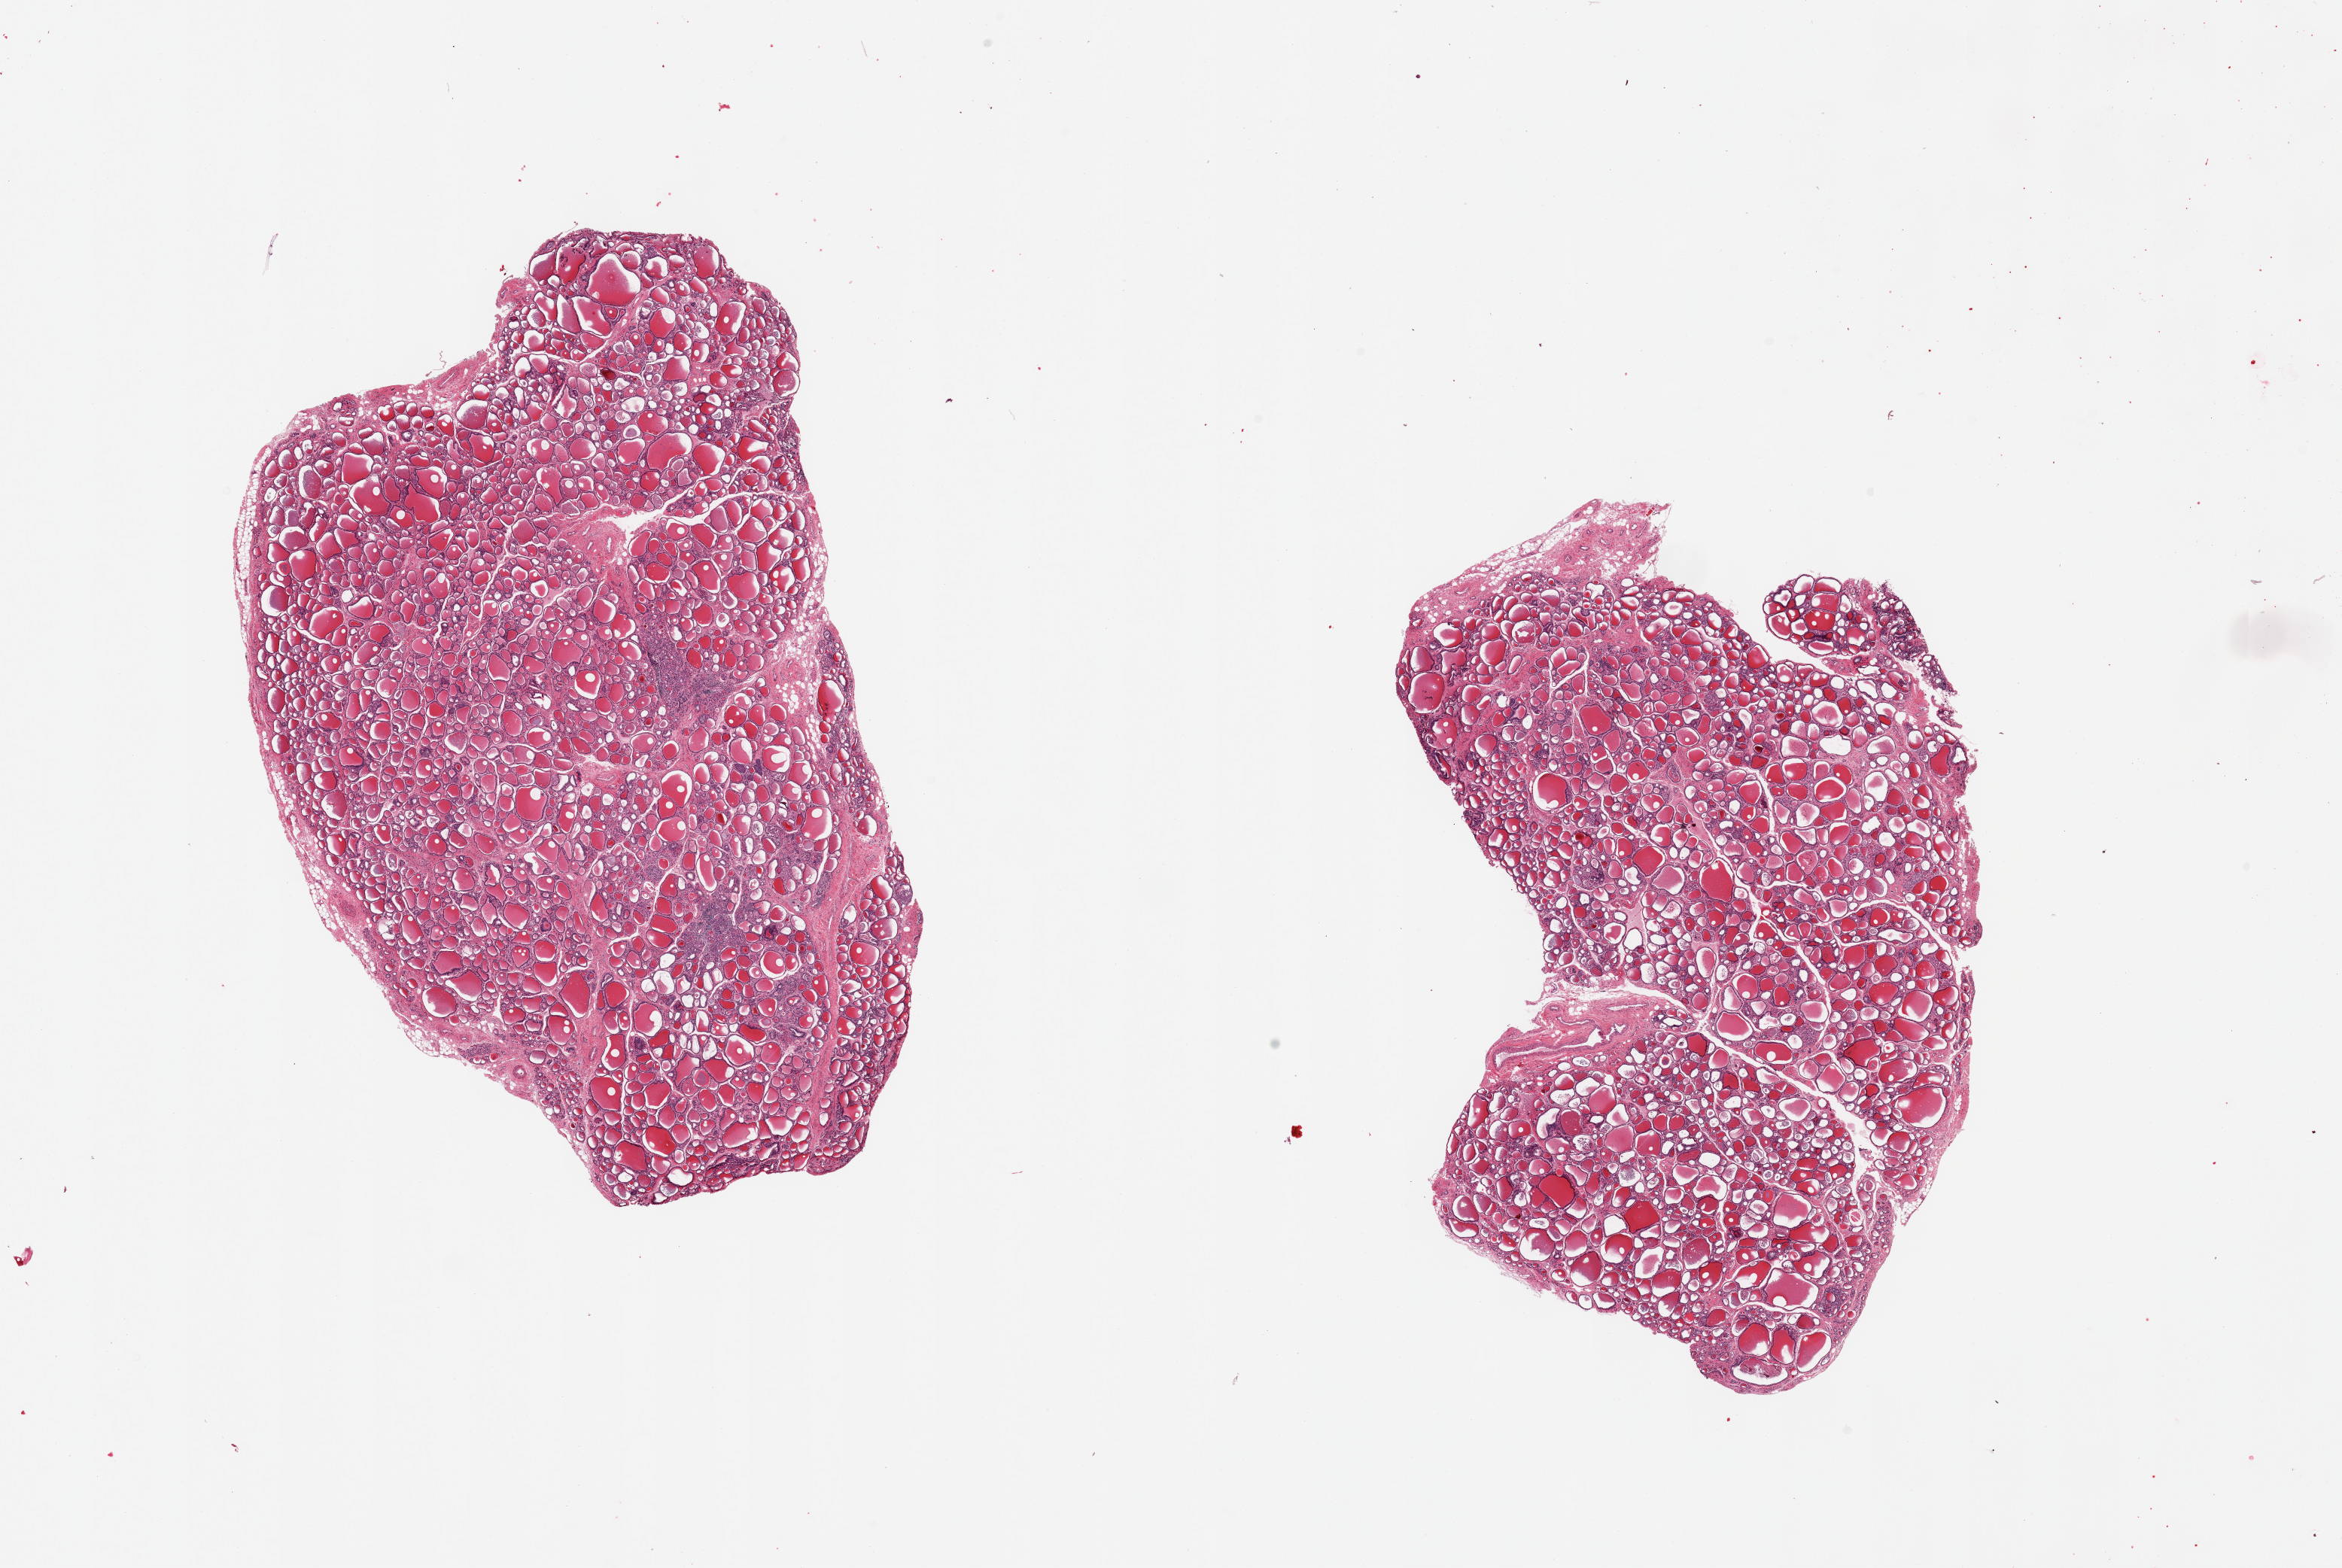
H&E whole-slide image, a low-resolution overview of the entire scanned area, about 24.6 x 16.5 mm. PAXgene-fixed, paraffin-embedded tissue. Target tissue: thyroid. Donor tissue sample. Donor sex: male.
Review note (as recorded): 2 pieces; small collections of lymphocytes.